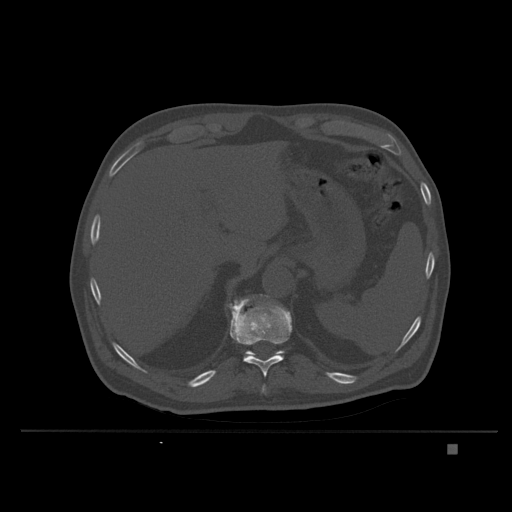
CT including the spine, one axial slice. Position 174 of 435 along the scan axis. Bone window (W 1800 / L 400 HU). 512 × 512 image matrix, field of view 434 × 434 mm. Male patient, age 73 years. From the clinical record (not read from this slice): primary cancer: skin.
Structures marked on this image (semi-automatically segmented with operator editing):
- T10 vertebra: bounding box (x1, y1, x2, y2) in pixels: (261, 384, 267, 394)
- T11 vertebra: (230, 296, 292, 377)
- T12 vertebra: (244, 350, 284, 357)